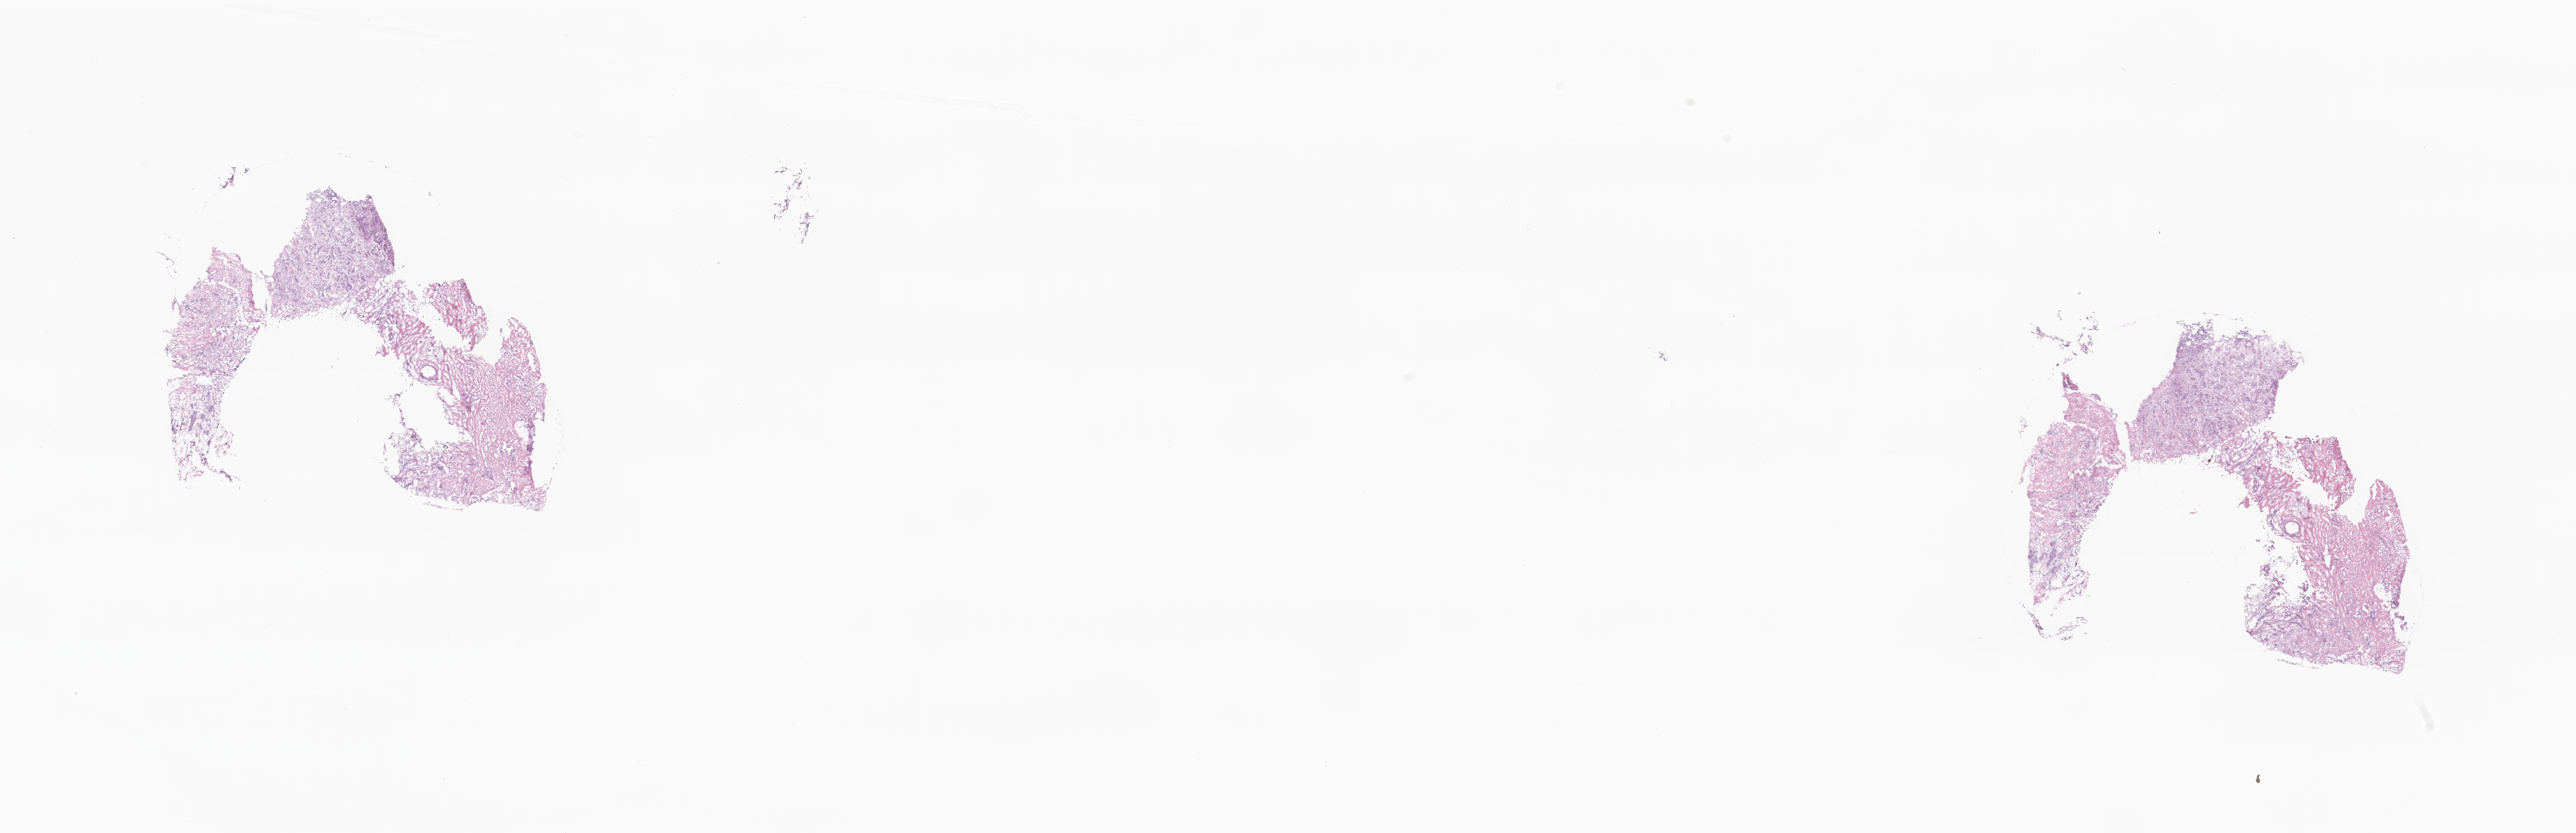
Whole-slide image, haematoxylin and eosin stain — low-resolution overview of the scanned area, about 29.5 x 9.5 mm; frozen section; specimen: primary tumor; anatomic site: breast (right). Patient: female, age at initial diagnosis 67 years.
Diagnosis: Infiltrating duct carcinoma, NOS.